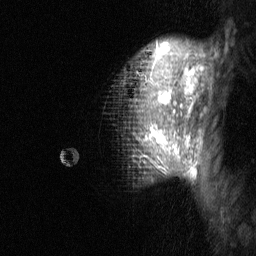
Breast MRI (dynamic contrast-enhanced), one sagittal slice; position 50 of 64 along the scan axis; dynamic contrast-enhanced study with each time point stored as its own series, time point 2 of 3 at this slice position (early post-contrast, ordered by acquisition time); 1.5 T; TE 4.8 ms, TR 27 ms; 2 mm slice thickness; 256 × 256 image matrix. Patient: female, 36 years. From the clinical record (not read from this slice): setting: breast cancer imaged before/during neoadjuvant chemotherapy; receptor status: HR-positive, HER2-negative.
Structures marked on this image (semi-automatically segmented with operator editing):
- analysis volume of interest (the breast-tissue region the enhancement analysis was run in; not a lesion): box from (x=67, y=37) to (x=208, y=184) px
- tumour enhancement mask (voxels above the 90 % enhancement threshold inside the analysis volume of interest): (x=151, y=43)–(x=201, y=177)